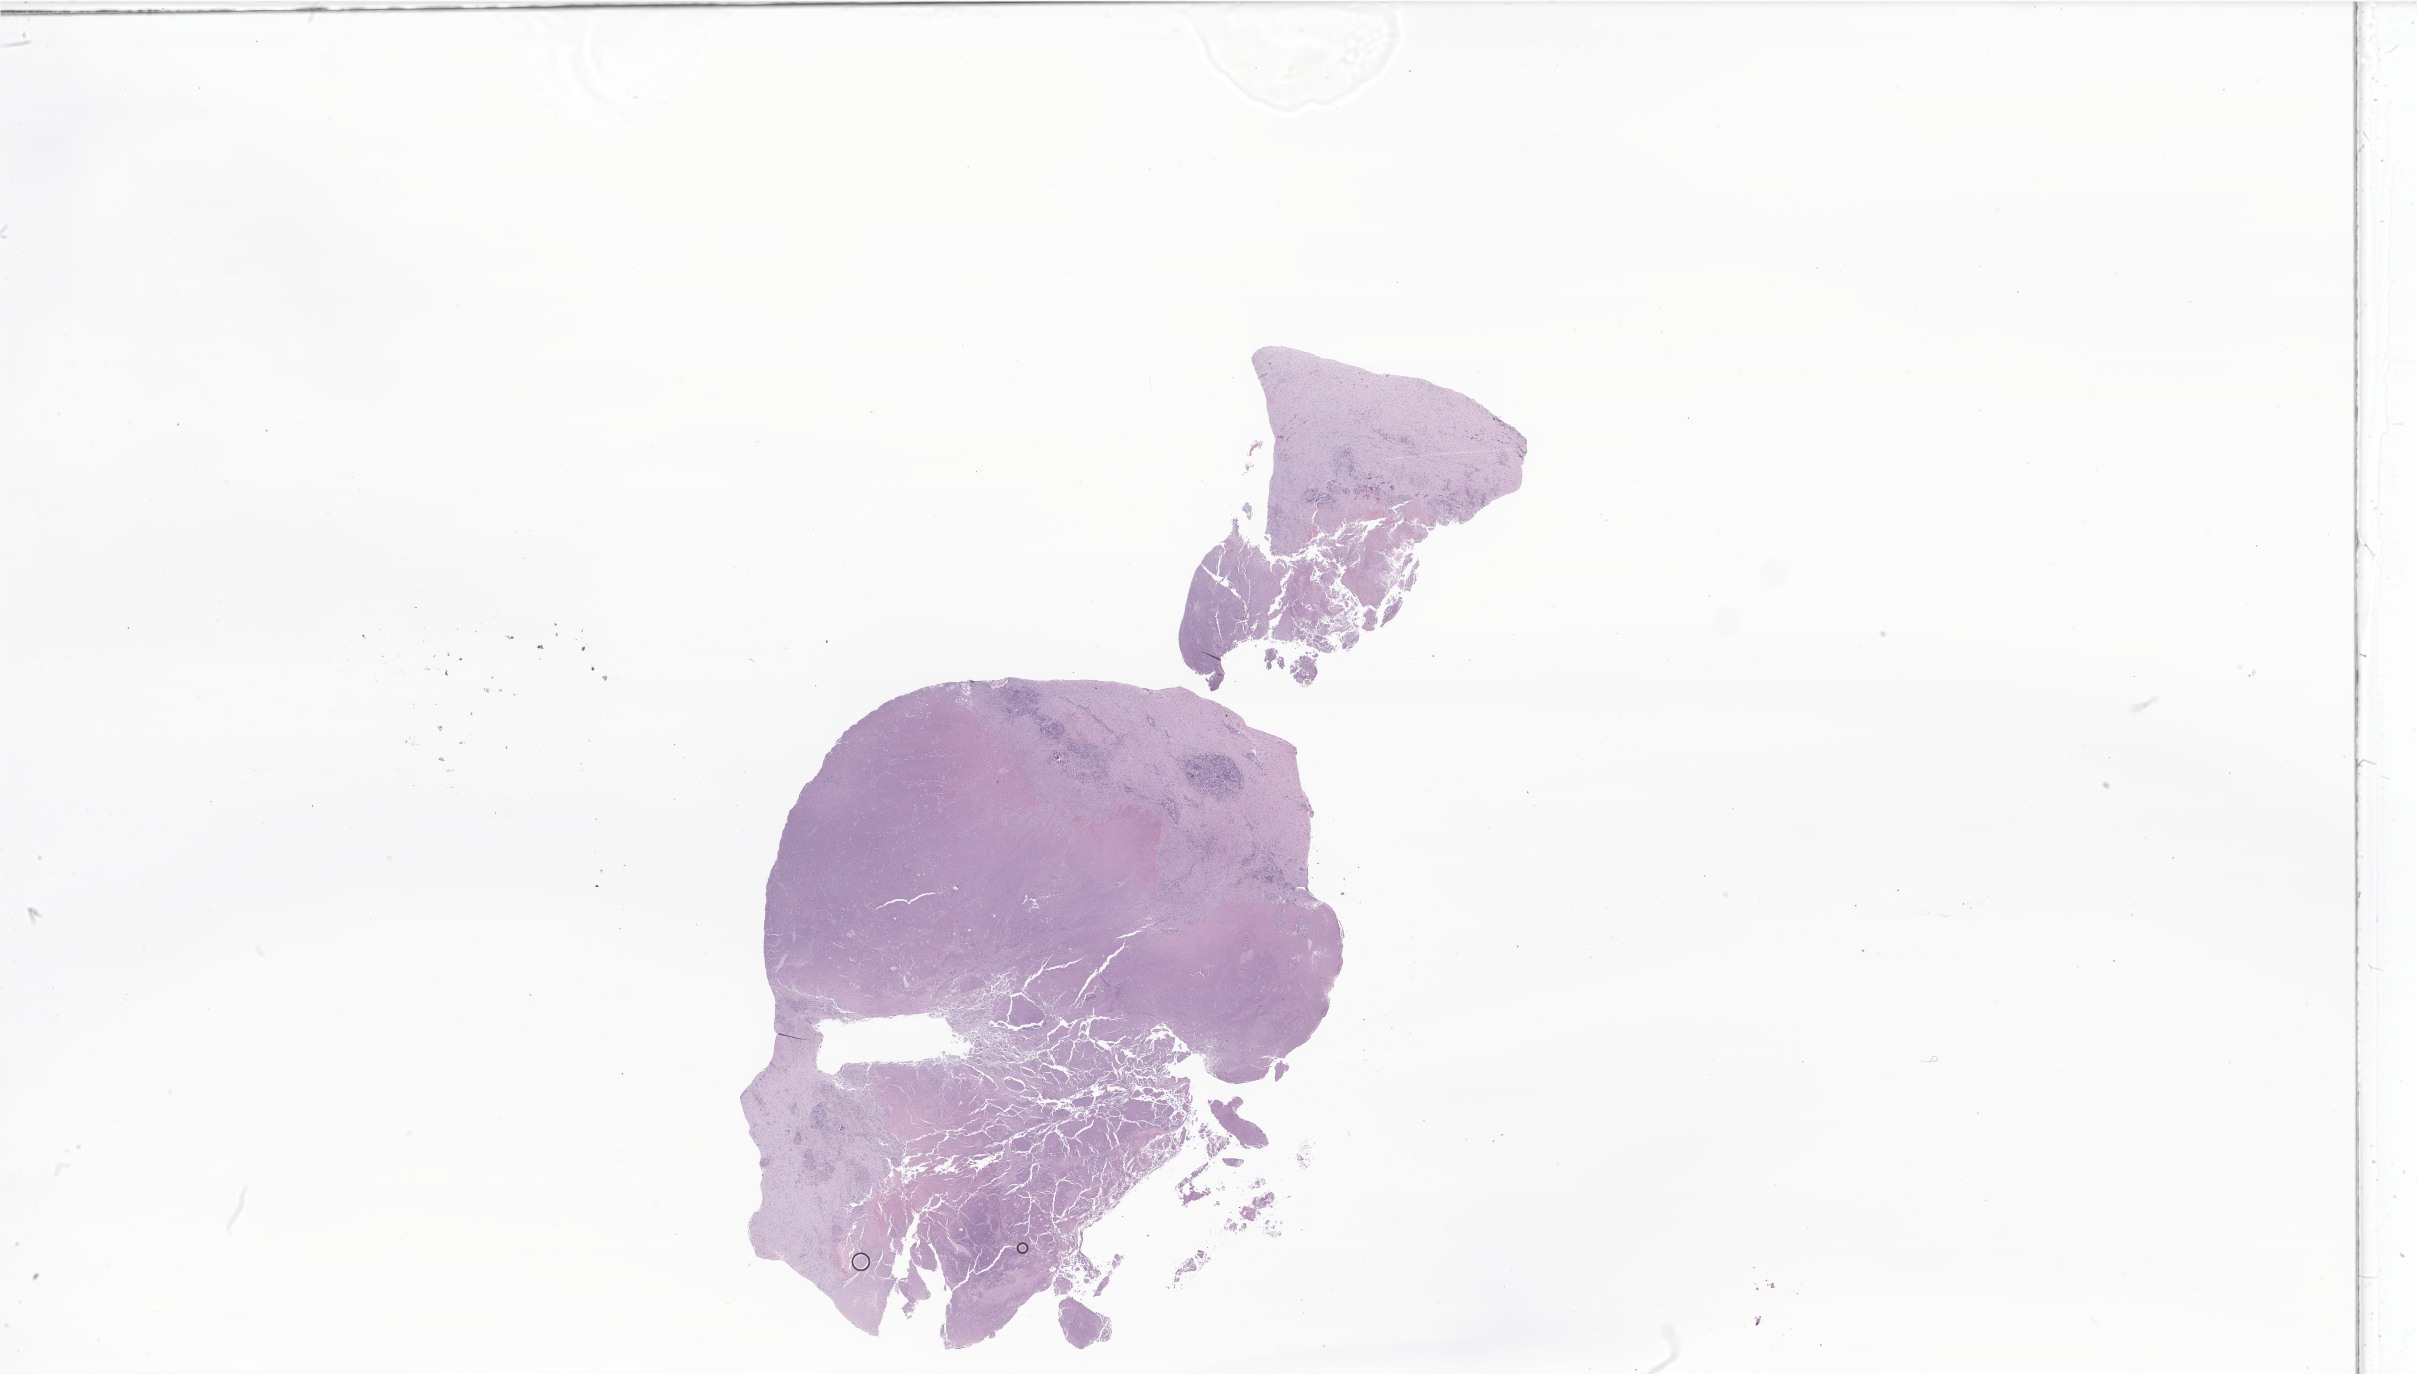
Digitized hematoxylin and eosin (H&E)-stained section of tumor tissue from the abdomen, whole scanned area (about 40.8 x 23.2 mm) shown as a low-resolution overview; formalin-fixed paraffin-embedded section. Patient: male, age 652 days (about 1.8 years).
• diagnosis (ICD-O-3 morphology term): Neoplasm, uncertain whether benign or malignant